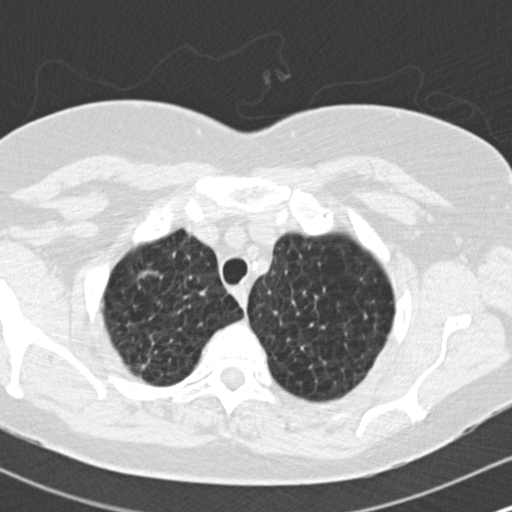
Chest CT (low-dose screening protocol), one axial image; first (baseline) screen; lung window (W 1500 / L -600 HU); 2 mm slice thickness; standard (soft-tissue) reconstruction kernel (B30f); 512 × 512 image matrix, field of view 310 × 310 mm. Female, age 73 years at enrolment.
Expert-annotated lung lesion, box from (x=126, y=252) to (x=172, y=291) px. The screening reader recorded 2 non-calcified nodules or masses ≥4 mm on this exam (right upper lobe, right upper lobe); which of them this box marks is not recorded. Official screen result: positive, change unspecified: nodule(s) >= 4 mm or enlarging nodule(s), mass(es), or other non-specific abnormalities suspicious for lung cancer. Participant outcome: lung cancer diagnosed 601 days after this screen (after the second annual screen) — adenocarcinoma, NOS, right upper lobe, moderately differentiated (G2), stage IB (AJCC 6th edition), 15 mm at pathology.